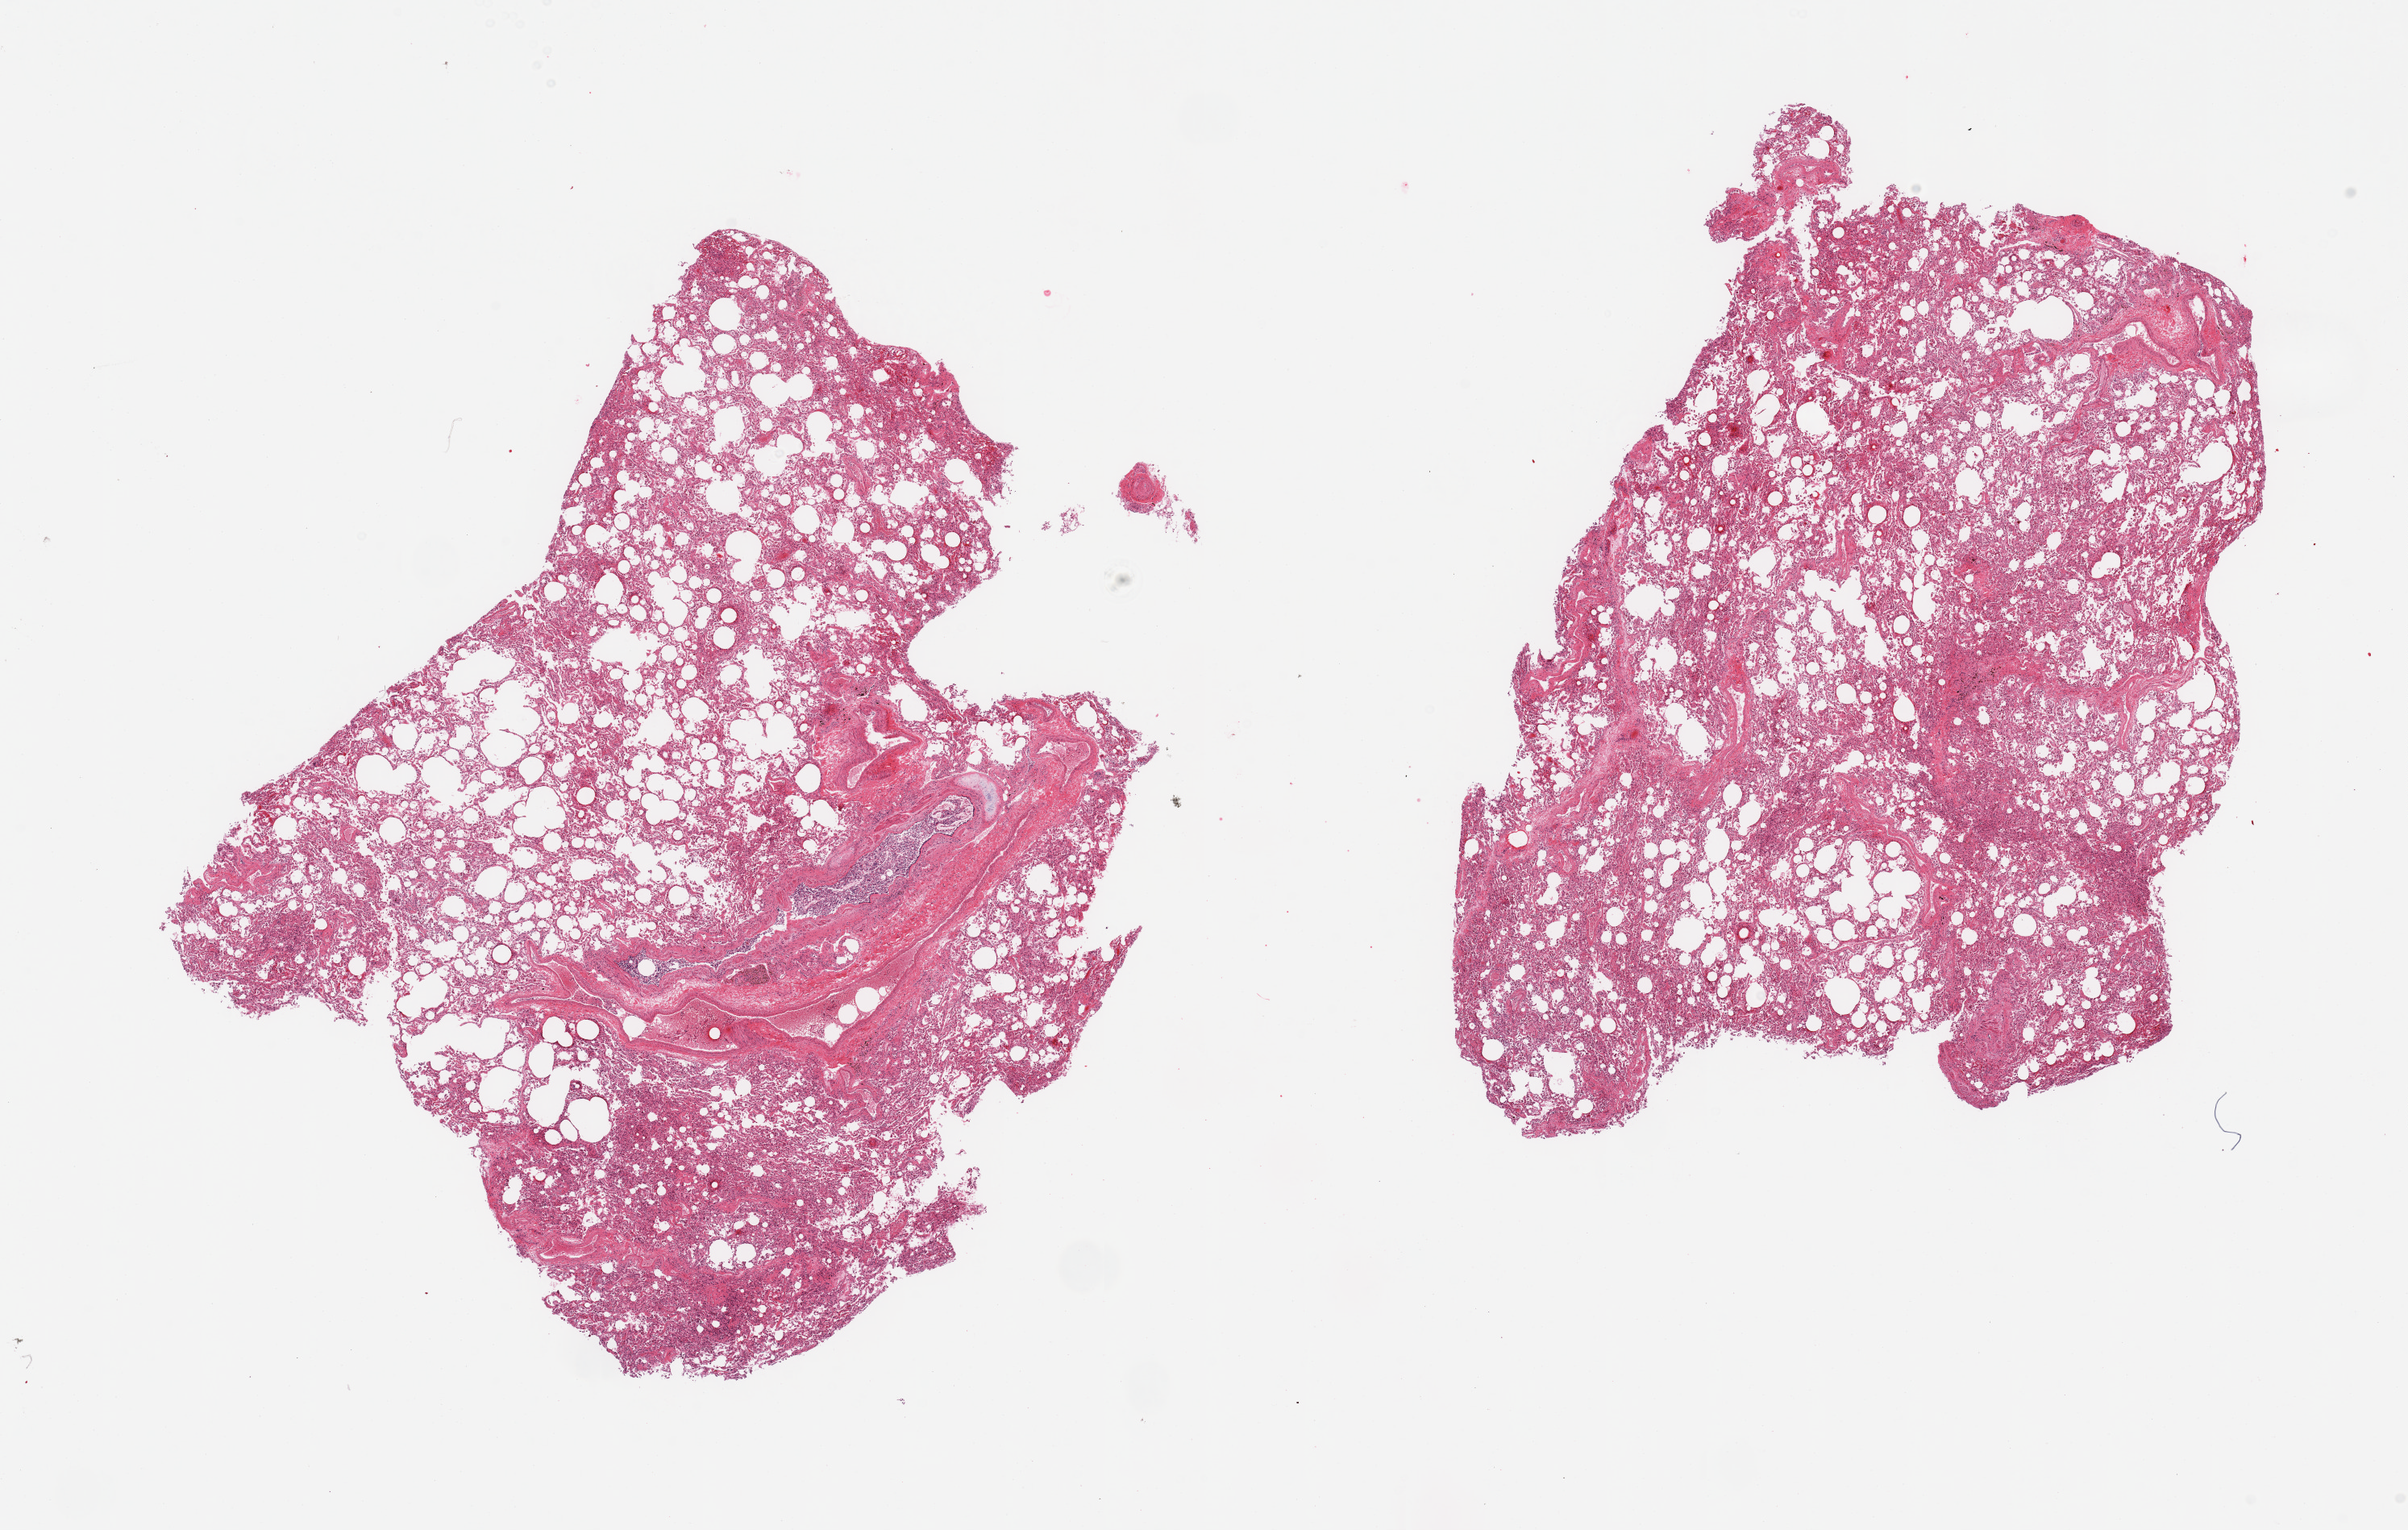
H&E whole-slide image — shown as a low-resolution overview of the whole scanned area (about 23.6 x 15.0 mm). PAXgene-fixed paraffin-embedded (PFPE) section. Section of lung (target tissue). Tissue donor sample. Donor sex: male.
Reviewer comment on this tissue sample: 2 pieces, moderate congestion.